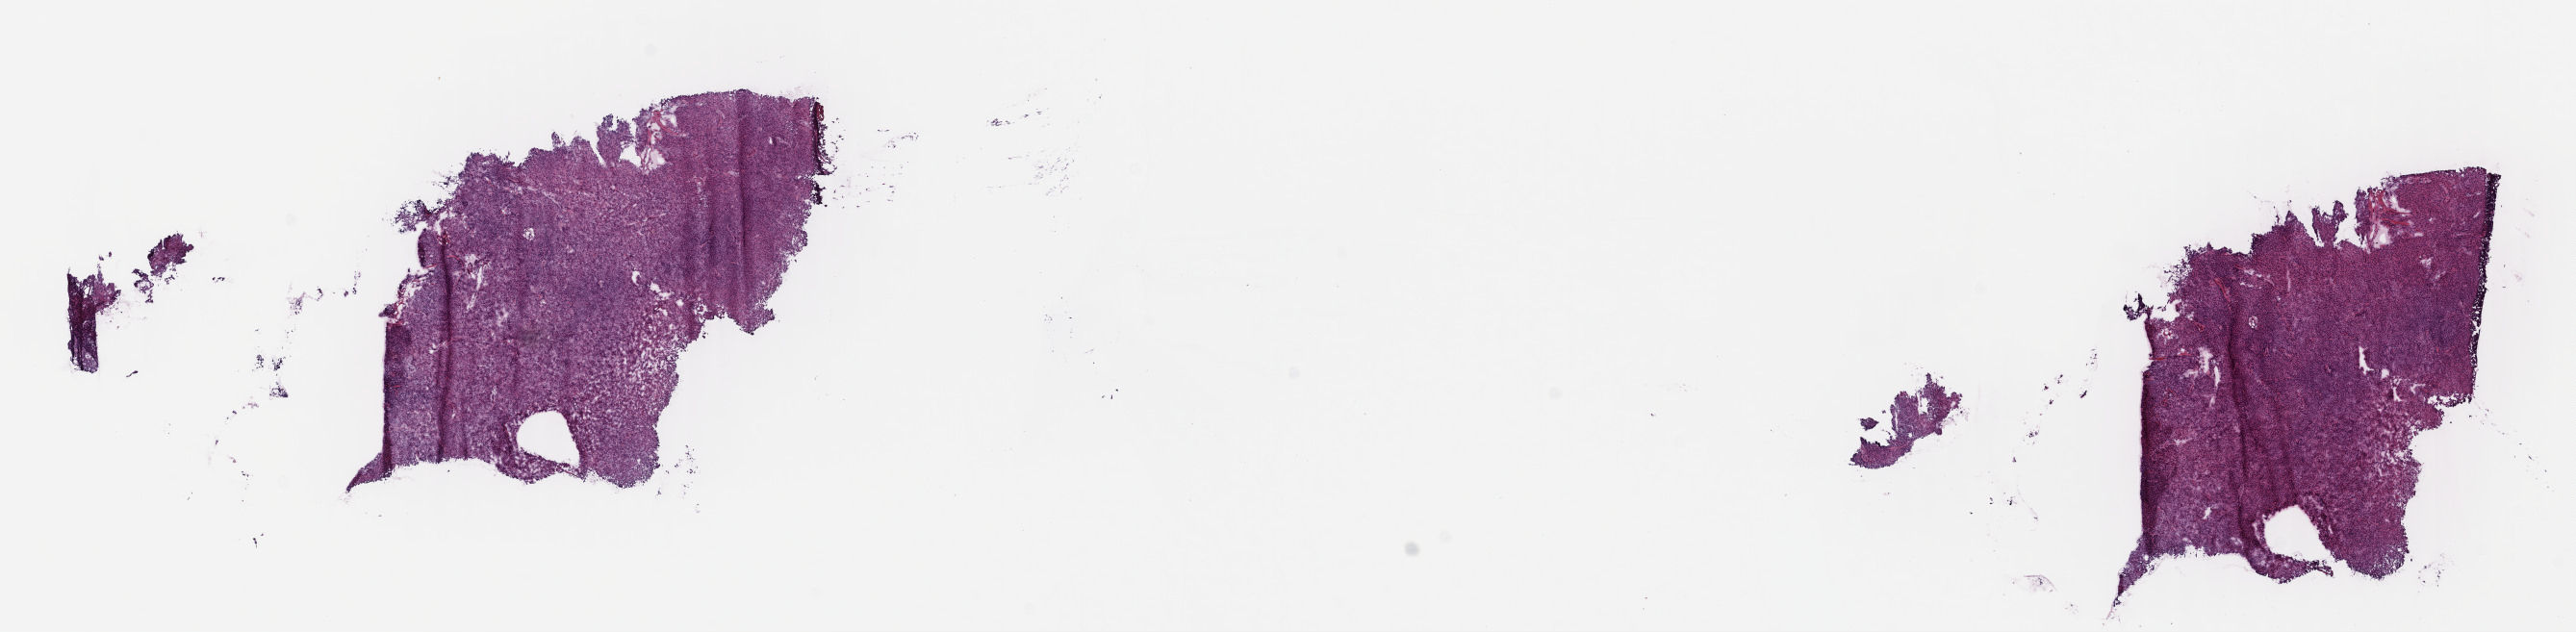
Digitized H&E-stained tissue section (whole slide), low-resolution overview of the scanned area, about 21.0 x 5.2 mm, frozen section from the top of the tissue portion, sample: recurrent tumour, uterus. Patient: female, age at initial diagnosis 62 years. Slide review estimates, as recorded: tumour cells 95%, tumour nuclei 100%, normal cells 0%, stromal cells 5%, necrosis 0%. Infiltration values recorded for this section: lymphocyte infiltration 0%, monocyte infiltration 0%, neutrophil infiltration 0%.
This section: recurrent tumour. Patient diagnosis: Leiomyosarcoma, NOS.